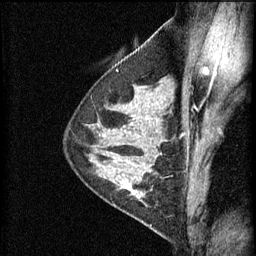
Breast MRI (dynamic contrast-enhanced), one sagittal slice. Slice 40 of 60 in the series (ordered by position). 3 images stored at this slice position (order not interpretable as contrast timing). 1.5 T. TE 4.2 ms, TR 11 ms. 2 mm slice thickness. 256 × 256 image matrix, field of view 180 × 180 mm. Patient: female, 29 years.
Annotated regions visible in this slice (semi-automatic segmentation, software-assisted and operator-edited):
- analysis volume of interest (the breast-tissue region the enhancement analysis was run in; not a lesion): bounding box [x1, y1, x2, y2] px = [105, 172, 169, 227]
- tumour enhancement mask (voxels above the 70 % enhancement threshold inside the analysis volume of interest): [114, 172, 153, 199]